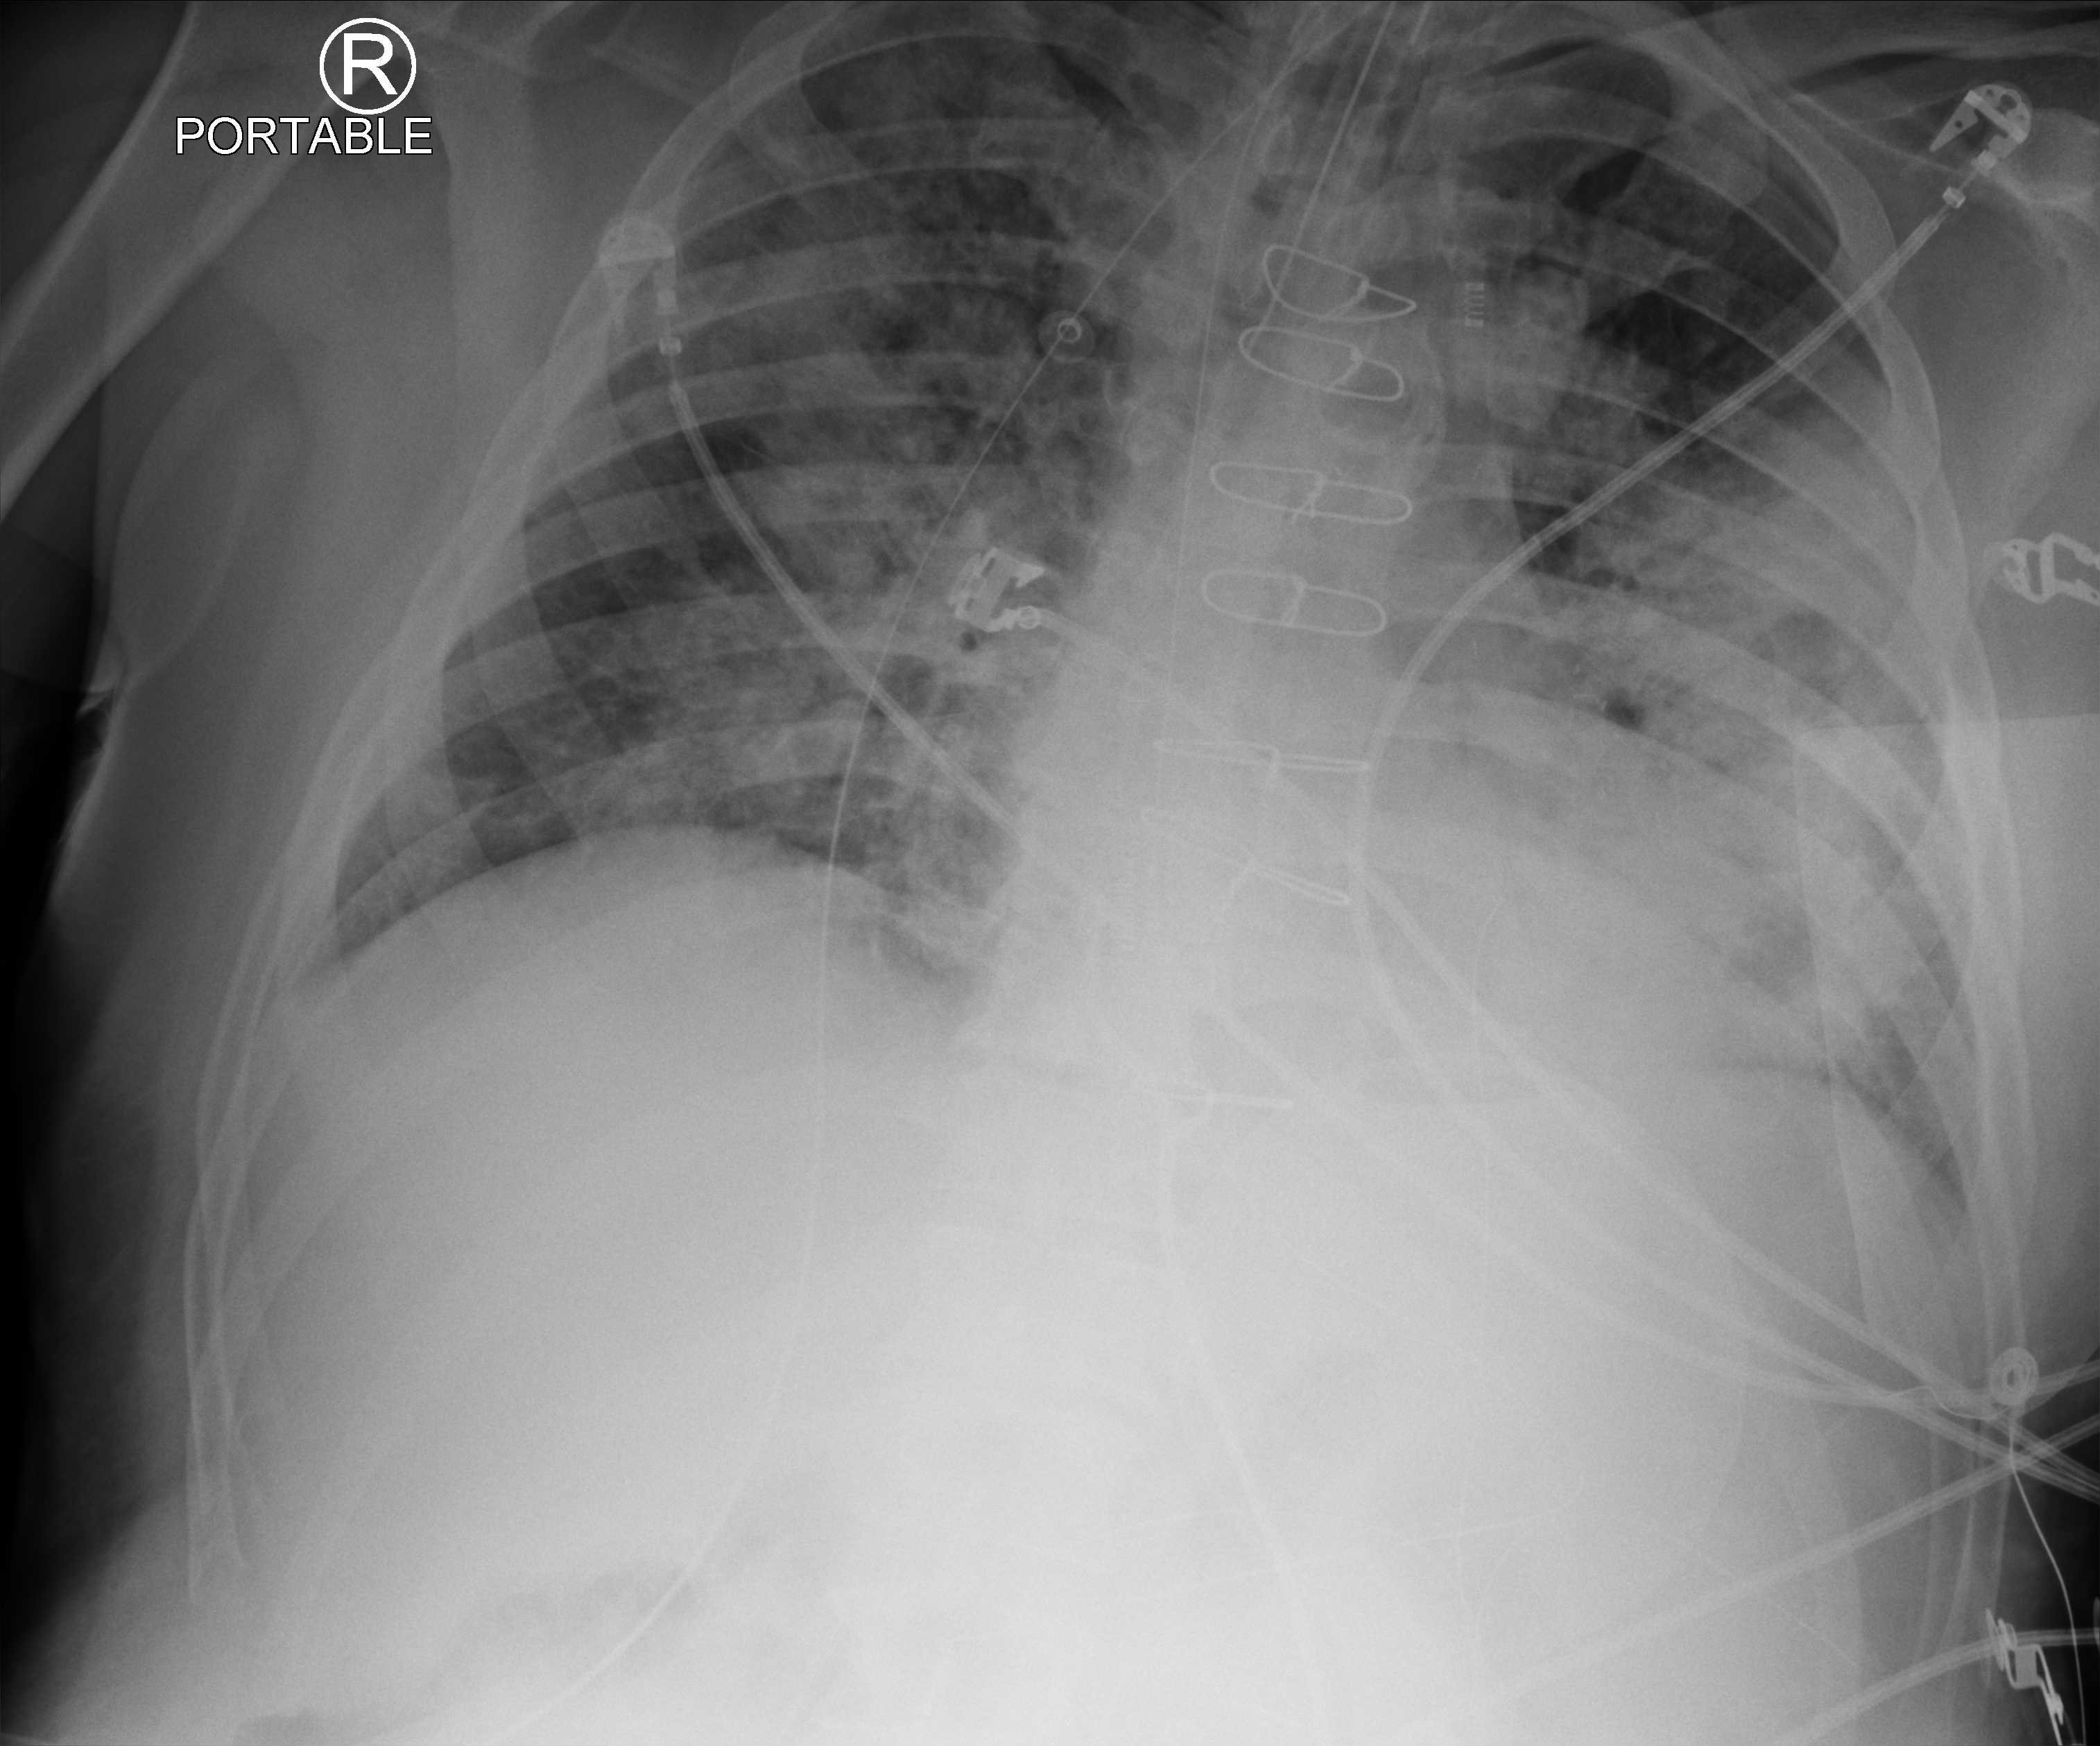
Portable chest radiograph, anteroposterior (AP) projection. Male patient hospitalised with COVID-19, age 60–74 years.
Admission-level facts for this patient (not findings on this image; timing relative to this image not recorded):
- mechanically ventilated during this hospital stay: yes
- admitted to intensive care during this hospital stay: yes